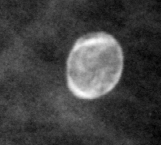
Crop from a digitized film mammogram around one marked abnormality; left breast; MLO view.
Finding: calcifications, morphology lucent center; BI-RADS assessment category 2; subtlety rating 5 on a 1 (subtle) to 5 (obvious) scale; benign without callback (not worked up further).